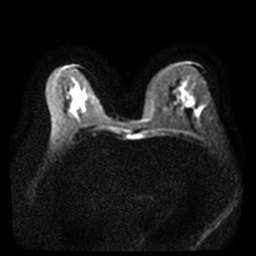
Breast MRI, one axial slice. Slice 20 of 40 in the series (ordered by position). Diffusion-weighted series; image 2 of 4 stored at this slice position (different b-values; order by instance number). 3 T. 5 mm slice thickness. 256 × 256 image matrix, field of view 360 × 360 mm. Female patient.
Outlined on this slice (expert manual segmentation):
- tumour on diffusion-weighted imaging: box from (x=184, y=99) to (x=194, y=106) px